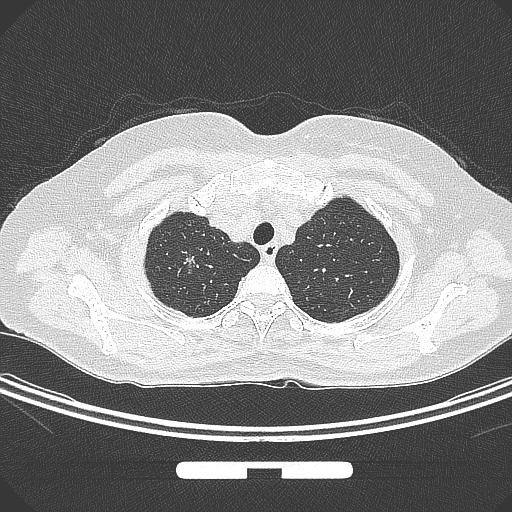
Chest CT, one axial slice. Lung window (W 1500 / L -600 HU). 1 mm slice thickness. 512 × 512 image matrix, field of view 369 × 369 mm. Patient: female, 58 years. From the clinical record (not read from this slice): clinical TNM (as recorded): T1b N0 M0; histopathological grade: G2-3.
Structures marked on this image (rectangle marked by the reading radiologist):
- lung tumour (recorded histology: adenocarcinoma): bounding box [x1, y1, x2, y2] px = [178, 250, 199, 277]